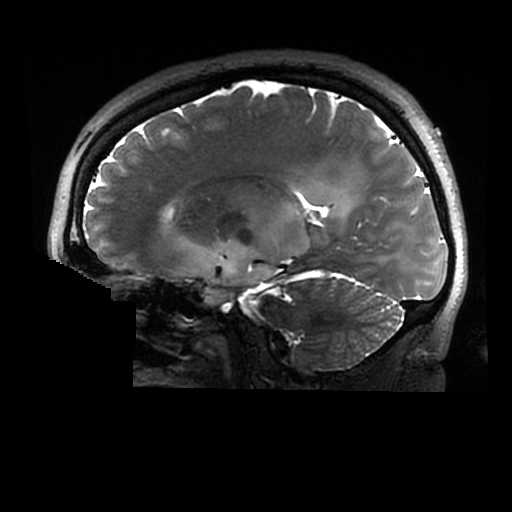
Brain MRI from a brain-tumour surgery series, one sagittal slice; slice 179 of 320 in the series (ordered by position); 0.6 mm slice thickness; 512 × 512 image matrix, field of view 240 × 240 mm. Case-level facts recorded for this patient, not image findings: histopathology: Astrocytoma; WHO grade: 2; IDH mutation: yes.
Structures marked on this image (outlined manually by an expert reader):
- tumour: bounding box [x1, y1, x2, y2] px = [182, 191, 352, 306]